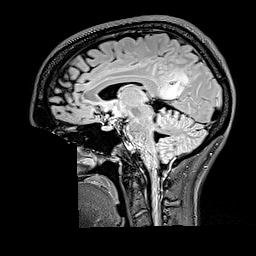
Brain MRI from a brain-tumour surgery series, one sagittal slice. Slice 91 of 176 in the series (ordered by position). T2 FLAIR. 256 × 256 image matrix. From the clinical record (not read from this slice): histopathology: Oligodendroglioma; WHO grade: 2; IDH mutation: yes.
Annotated regions visible in this slice (outlined manually by an expert reader):
- tumour: bounding box <160,73,189,98> (left, top, right, bottom; pixels)